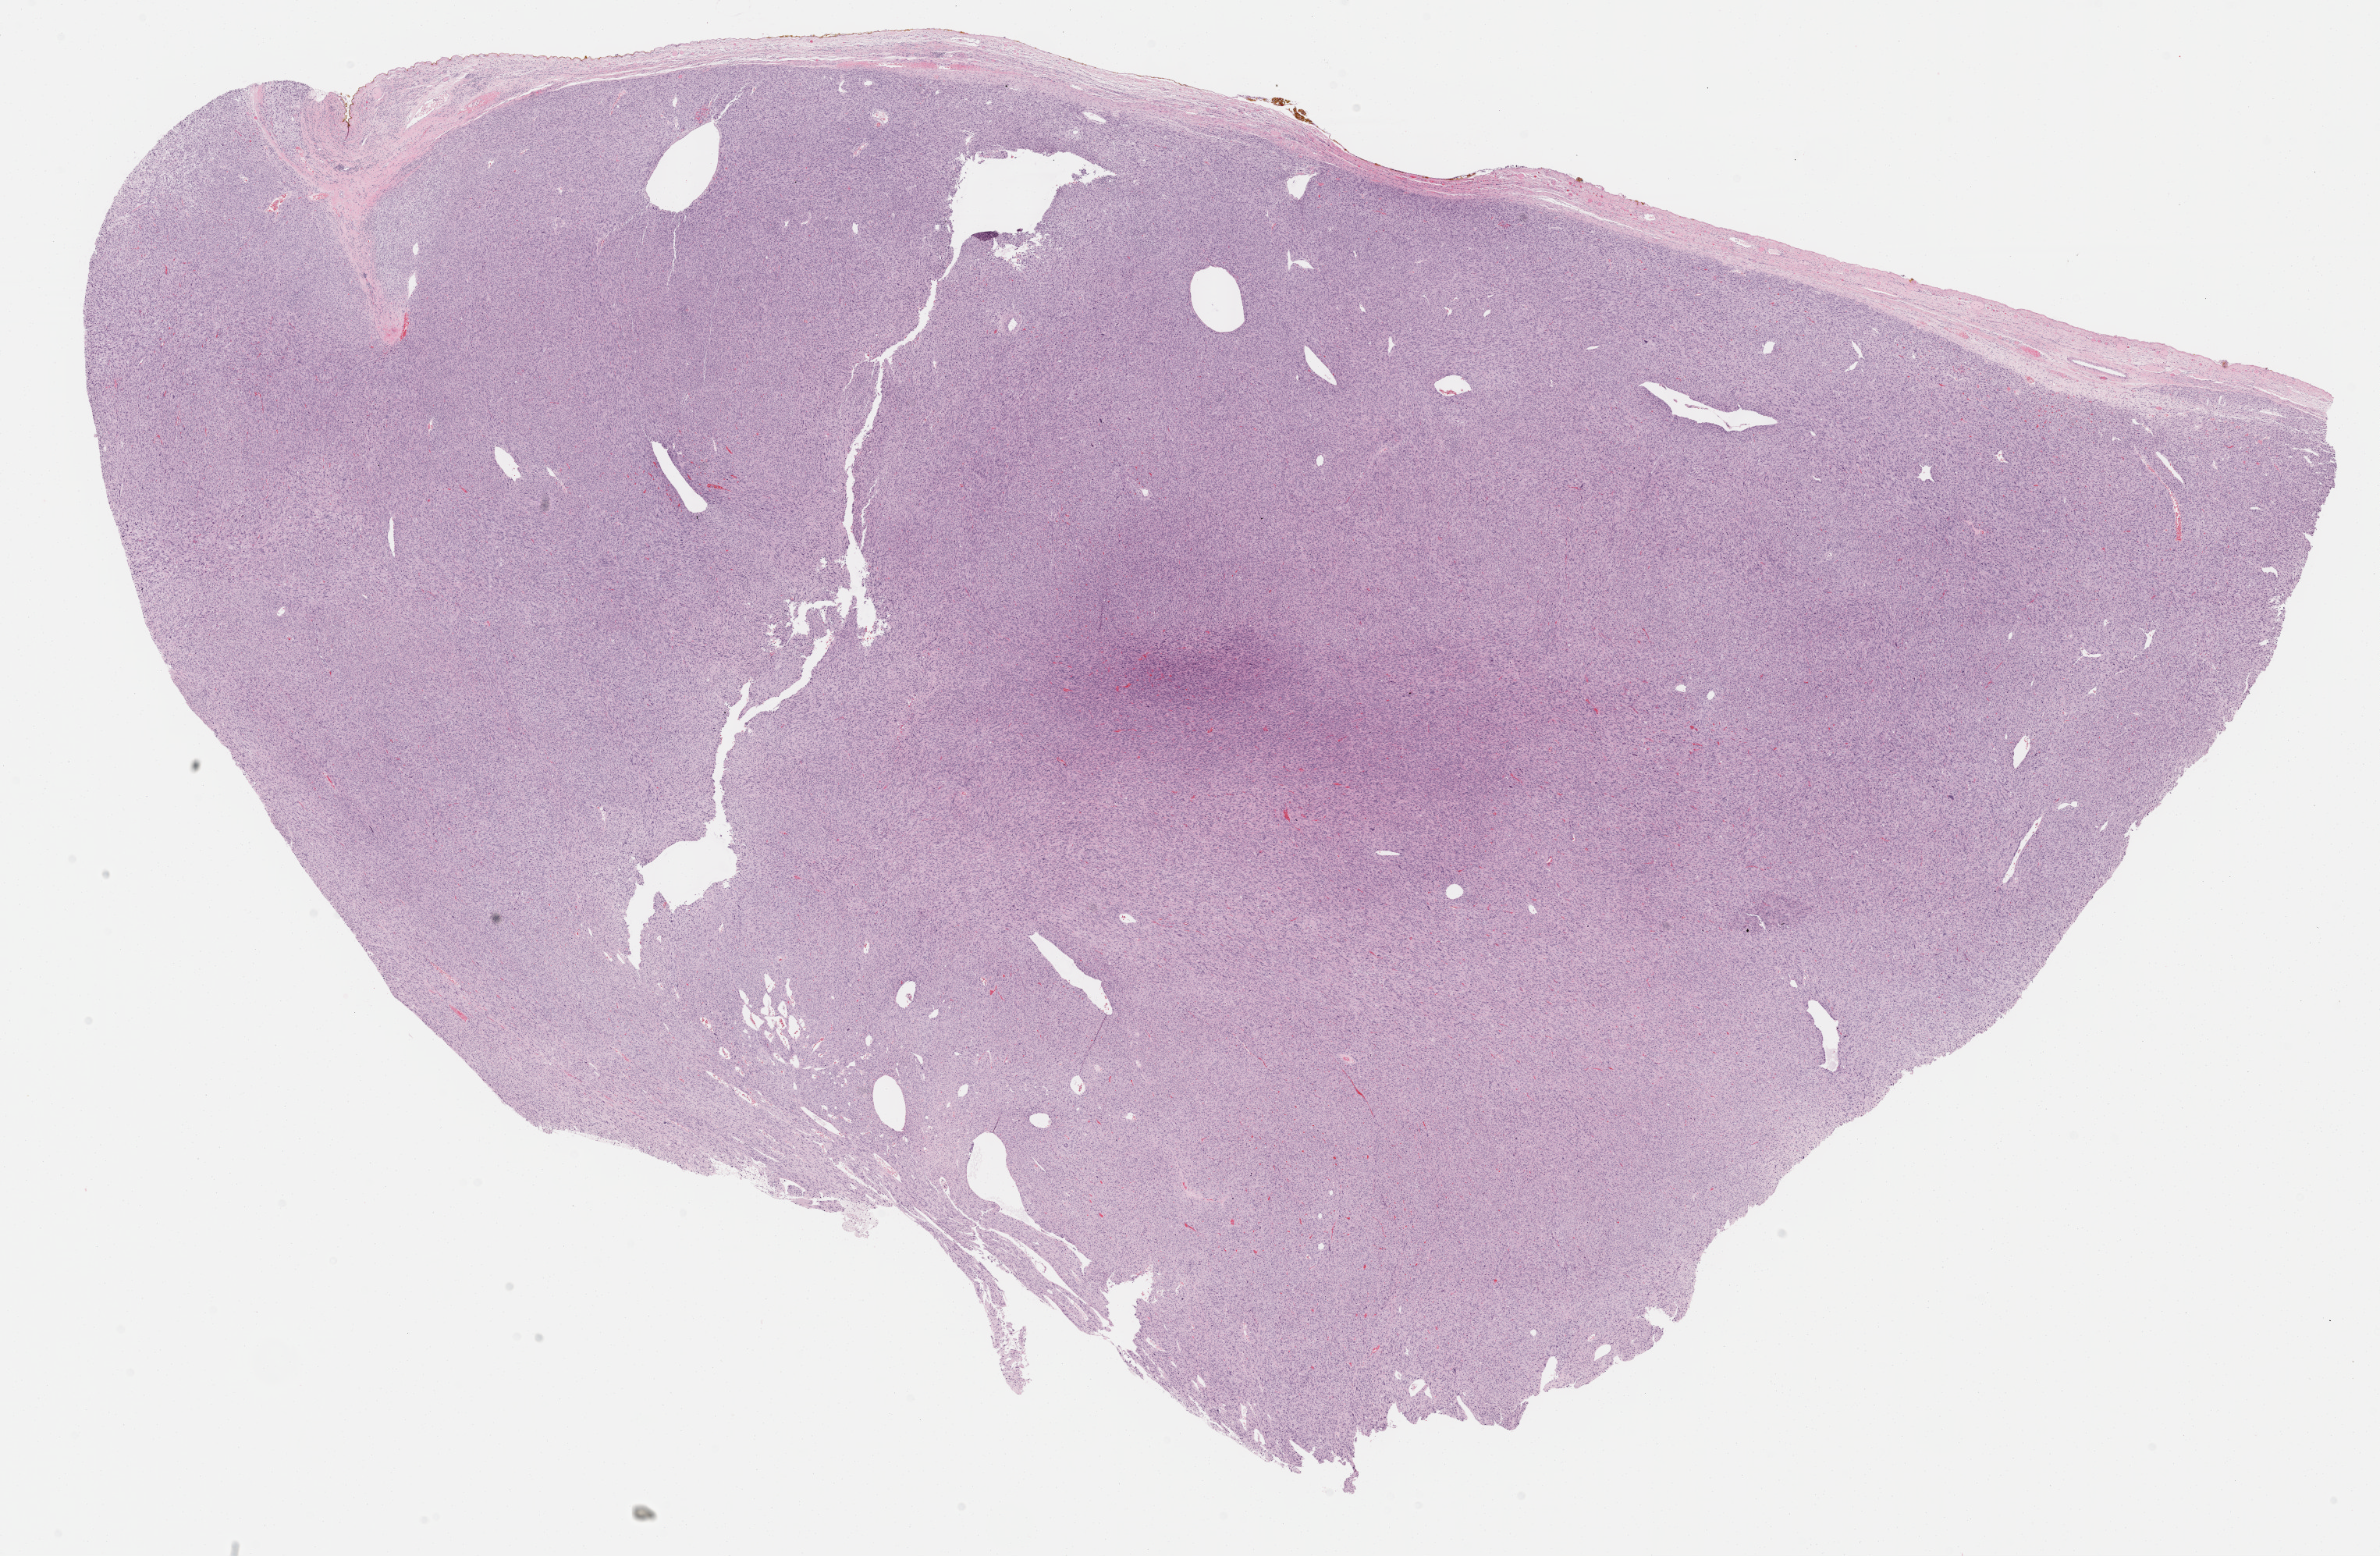
Digitized Hematoxylin and eosin (H&E) stained tissue section (whole slide), whole scanned area (about 24.7 x 16.1 mm) shown as a low-resolution overview; FFPE section; retroperitoneum and peritoneum, primary tumour sample. Female, age 78 years at initial diagnosis.
Pathologic diagnosis: Dedifferentiated liposarcoma (retroperitoneum).